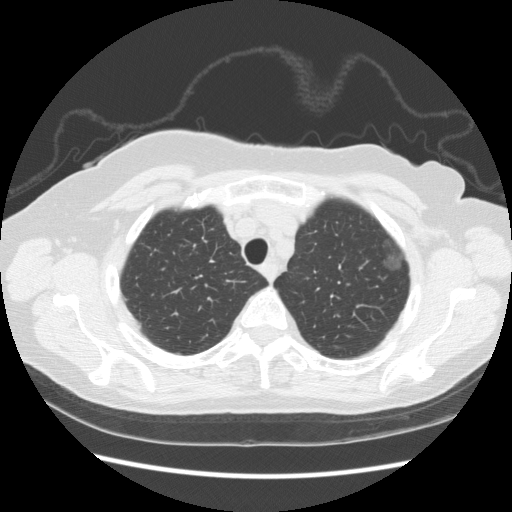
Low-dose screening chest CT, axial slice, baseline screening round, lung window (W 1500 / L -600 HU), 2.5 mm slice thickness. Female participant, aged 73 years at enrolment.
Expert reader's lesion annotation, bounding box [x1, y1, x2, y2] px = [372, 231, 414, 278]. The screening reader recorded 3 non-calcified nodules or masses ≥4 mm on this exam (left upper lobe, left upper lobe, left upper lobe); which of them this box marks is not recorded. Lung cancer was diagnosed 445 days after this screen: bronchiolo-alveolar adenocarcinoma, NOS, left upper lobe, well differentiated (G1), stage IA (AJCC 6th edition), 10 mm at pathology.